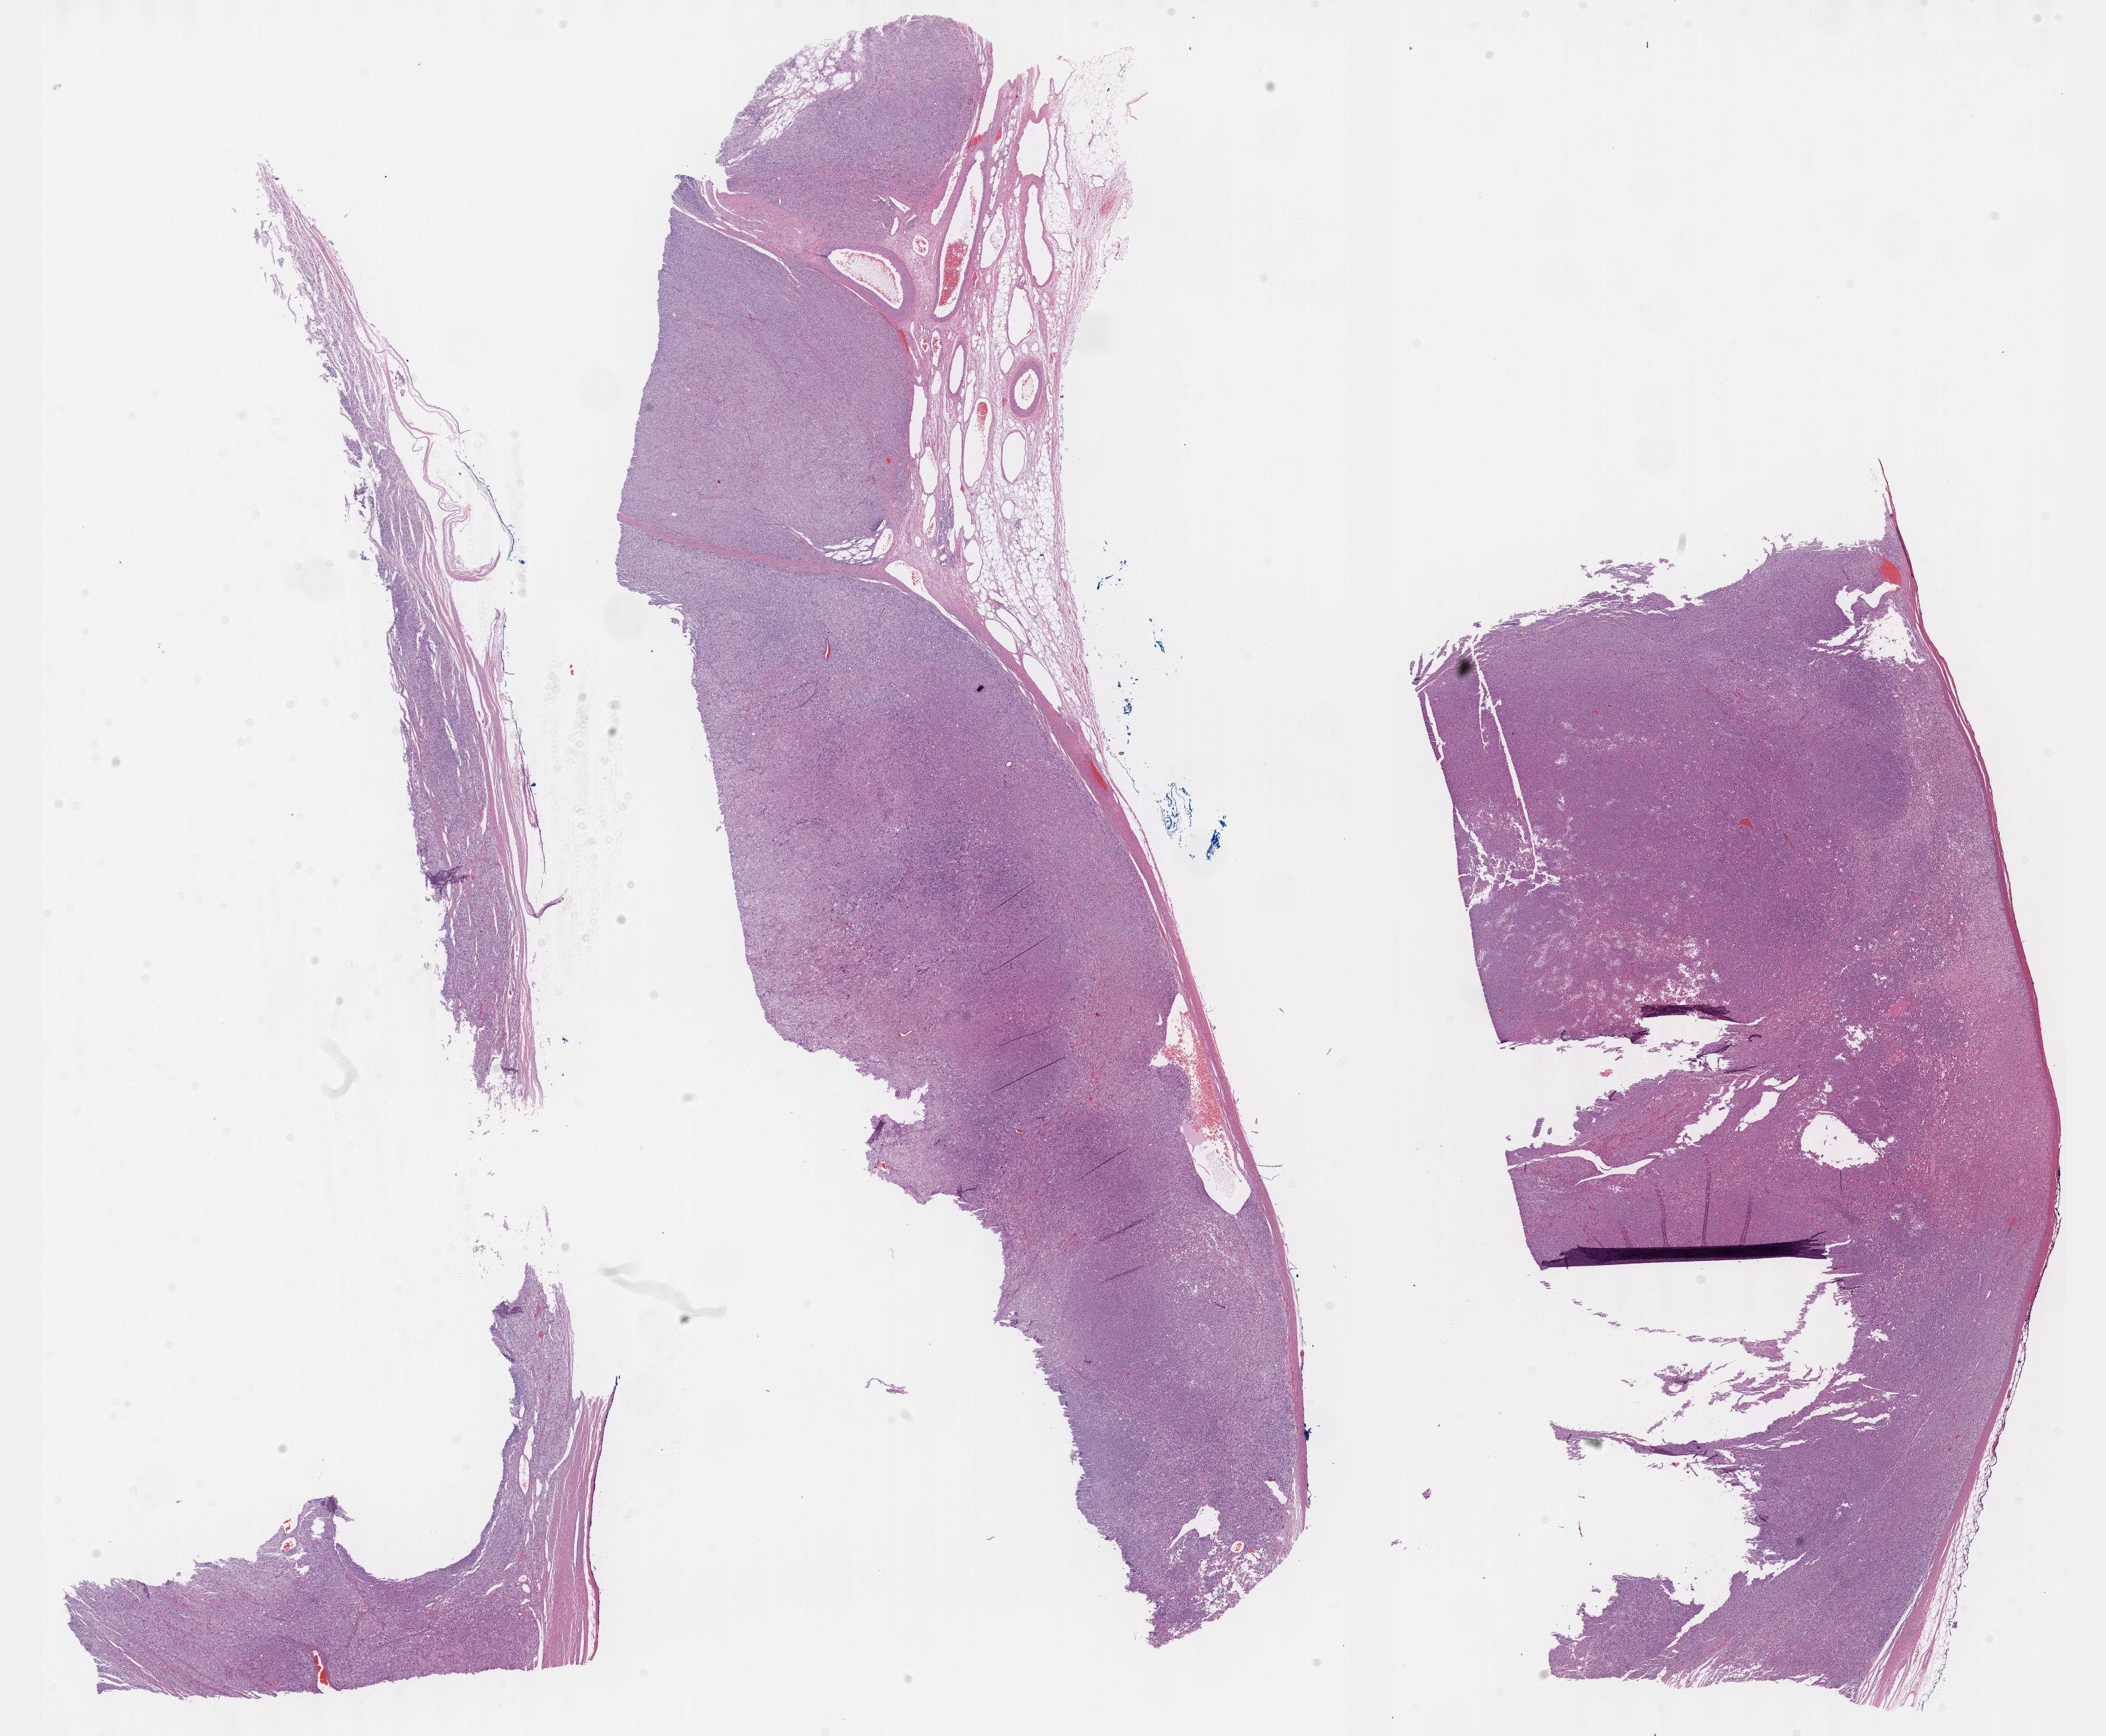
Whole-slide histology image, H&E-stained, shown as a low-resolution overview of the whole scanned area (about 25.1 x 20.7 mm, acquisition: 40x scan). Formalin-fixed paraffin-embedded (FFPE) diagnostic section. Sample: primary tumour, adrenal cortex. Patient: female, age at initial diagnosis 53 years.
• lymph nodes positive (case pathology): 3 of 3 examined
• pathologic diagnosis: Adrenal cortical carcinoma
• laterality: left